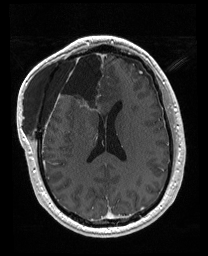
Brain MRI from a brain-tumour surgery series, one axial slice; slice 77 of 176 in the series (ordered by position); T1-weighted post-contrast; 1 mm slice thickness; 208 × 256 image matrix. Case-level facts recorded for this patient, not image findings: histopathology: Astrocytoma; WHO grade: 4; IDH mutation: yes.
Annotated regions visible in this slice (outlined manually by an expert reader):
- previous resection cavity: bounding box (x1, y1, x2, y2) in pixels: (56, 52, 106, 111)